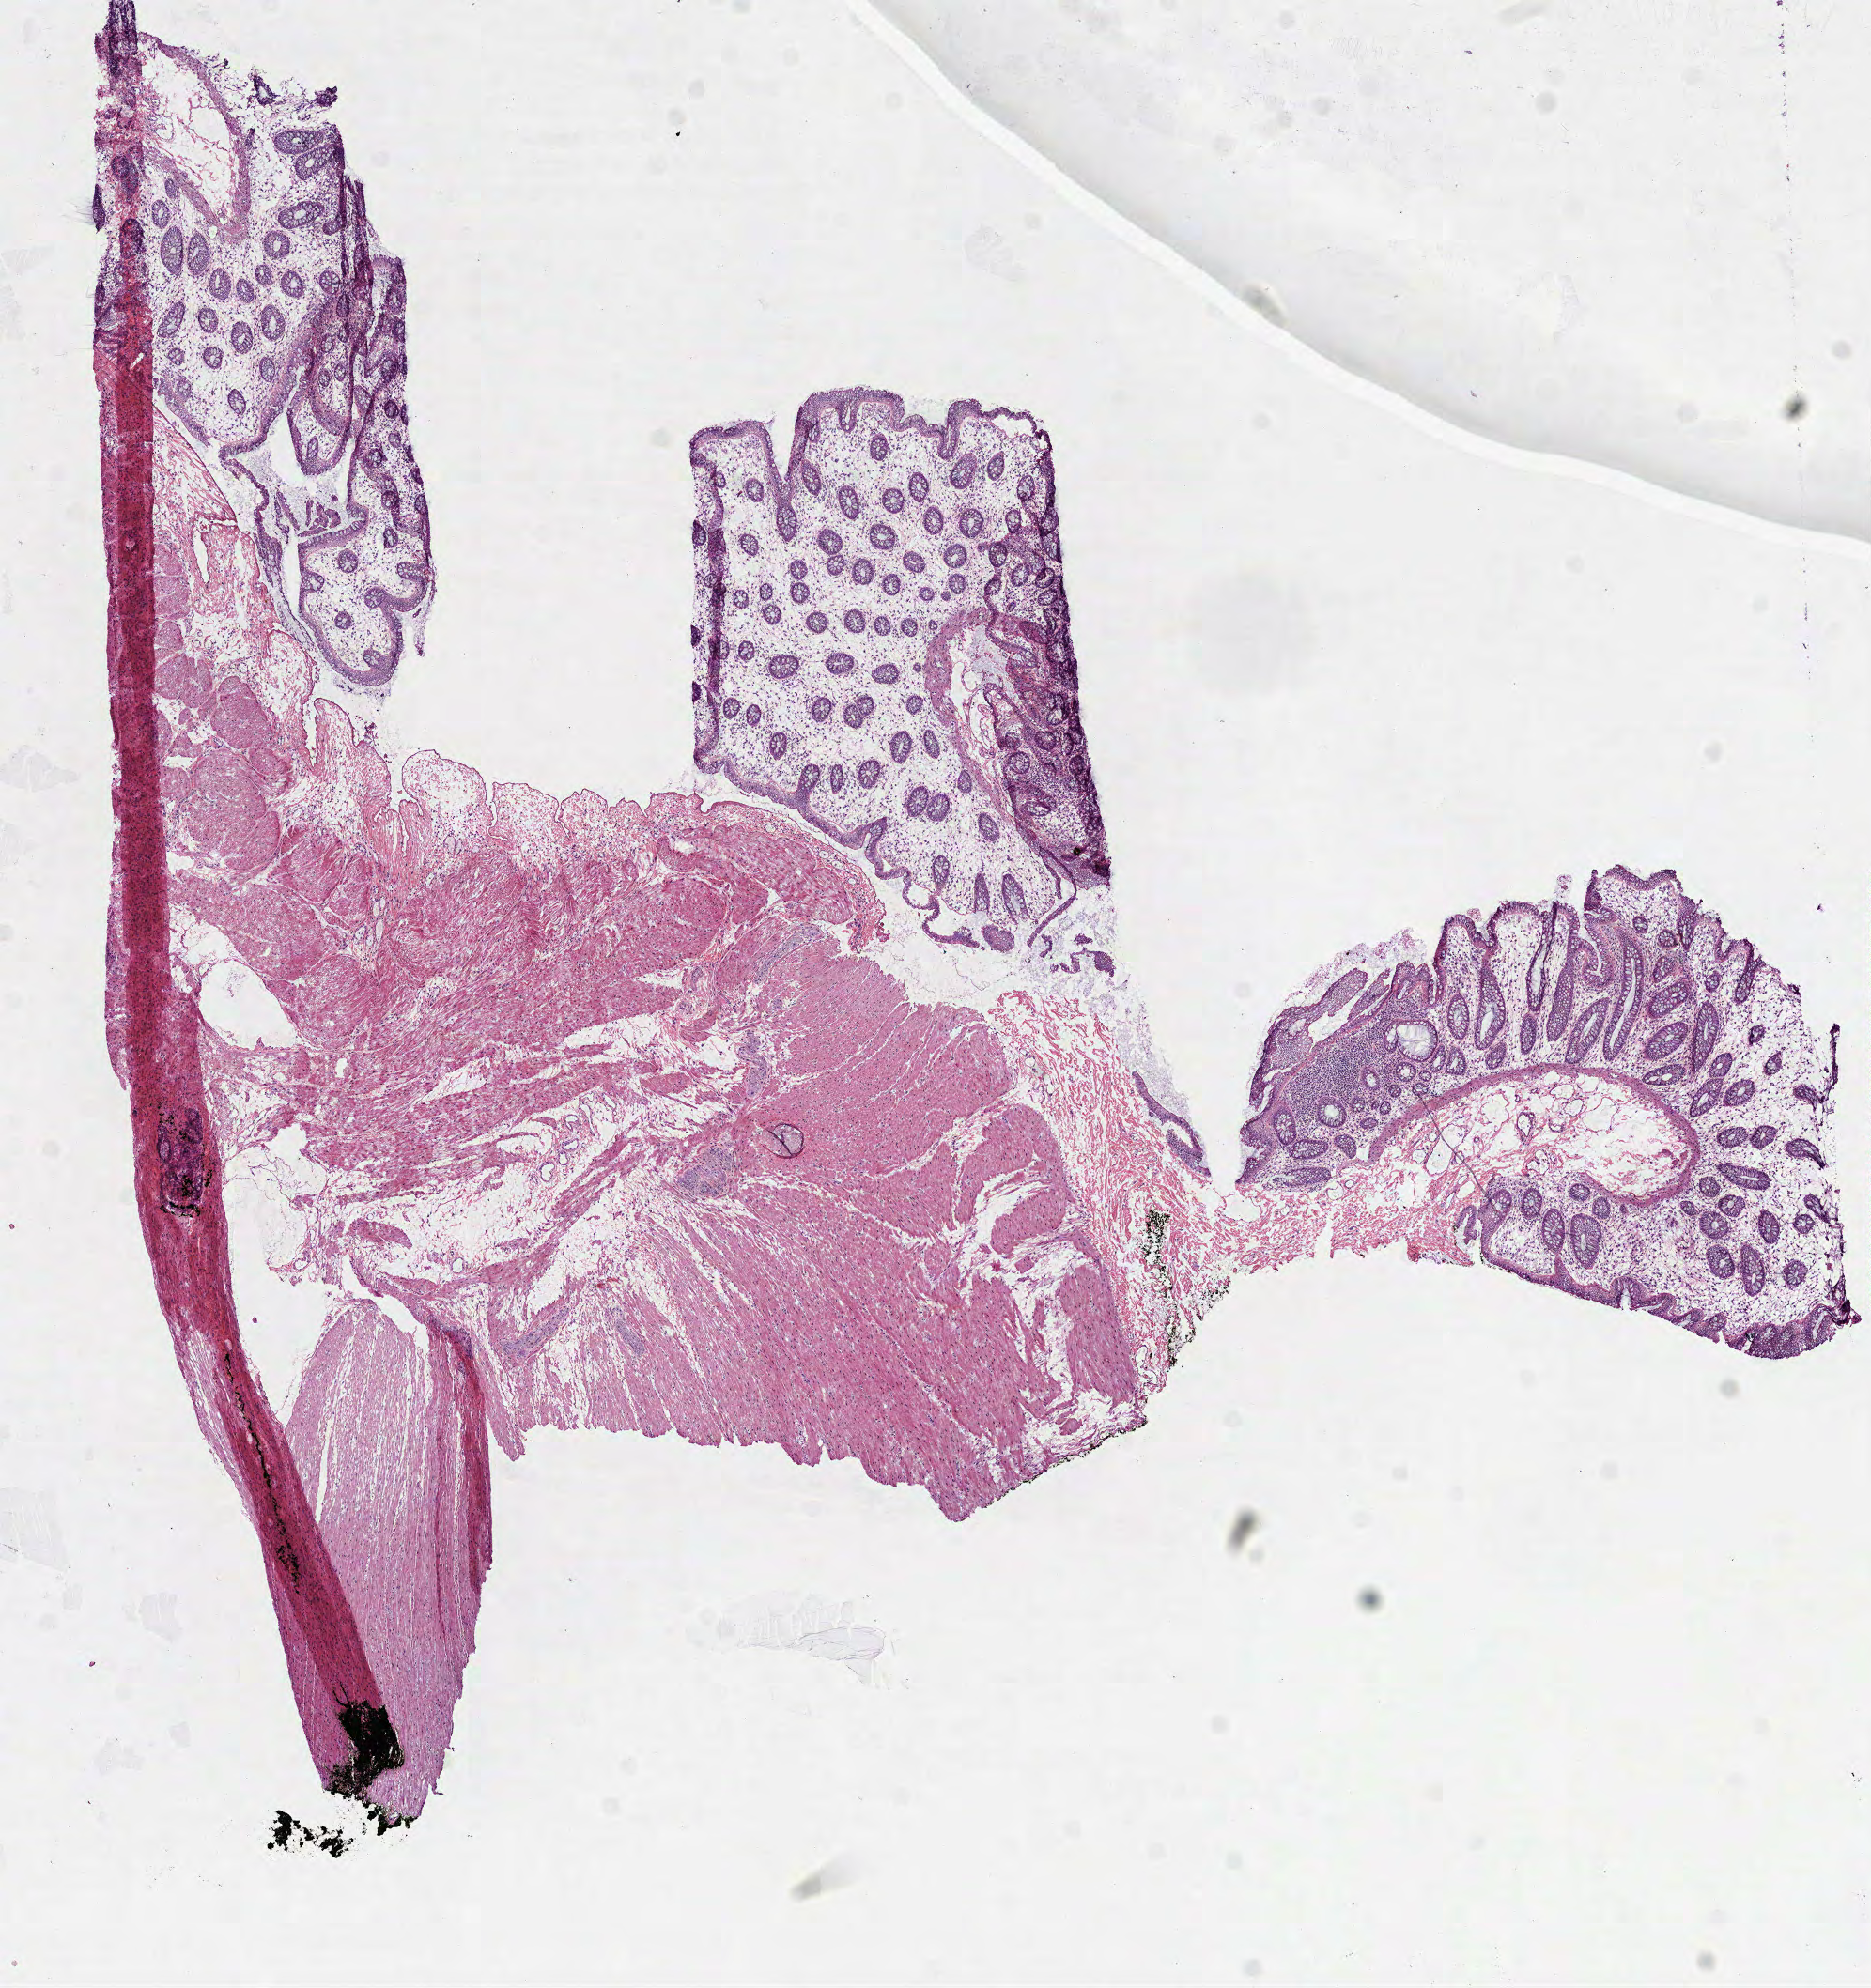
Digitized H&E tissue section (whole slide) — whole scanned area (about 8.0 x 8.5 mm) shown as a low-resolution overview. Frozen section from the top of the tissue portion. Solid tissue normal (non-tumour tissue) sample from the rectum. Male, age 50 years at initial diagnosis.
This section: solid tissue normal sample (biorepository sample class). Patient diagnosis: Adenocarcinoma, NOS (rectosigmoid junction).